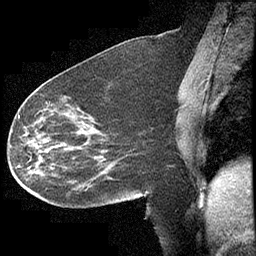
Breast MRI (dynamic contrast-enhanced), one sagittal slice; position 173 of 232 along the scan axis; dynamic contrast-enhanced study with each time point stored as its own series, time point 2 of 4 at this slice position (early post-contrast, ordered by acquisition time); 1.5 T; TE 4.2 ms, TR 6.7 ms; 256 × 256 image matrix. Female patient, age 63 years. From the clinical record (not read from this slice): setting: breast cancer imaged before/during neoadjuvant chemotherapy; receptor status: triple-negative.
Outlined on this slice (semi-automatically segmented with operator editing):
- analysis volume of interest (the breast-tissue region the enhancement analysis was run in; not a lesion): bounding box <13,90,140,209> (left, top, right, bottom; pixels)
- tumour enhancement mask (voxels above the 70 % enhancement threshold inside the analysis volume of interest): <18,115,79,169>